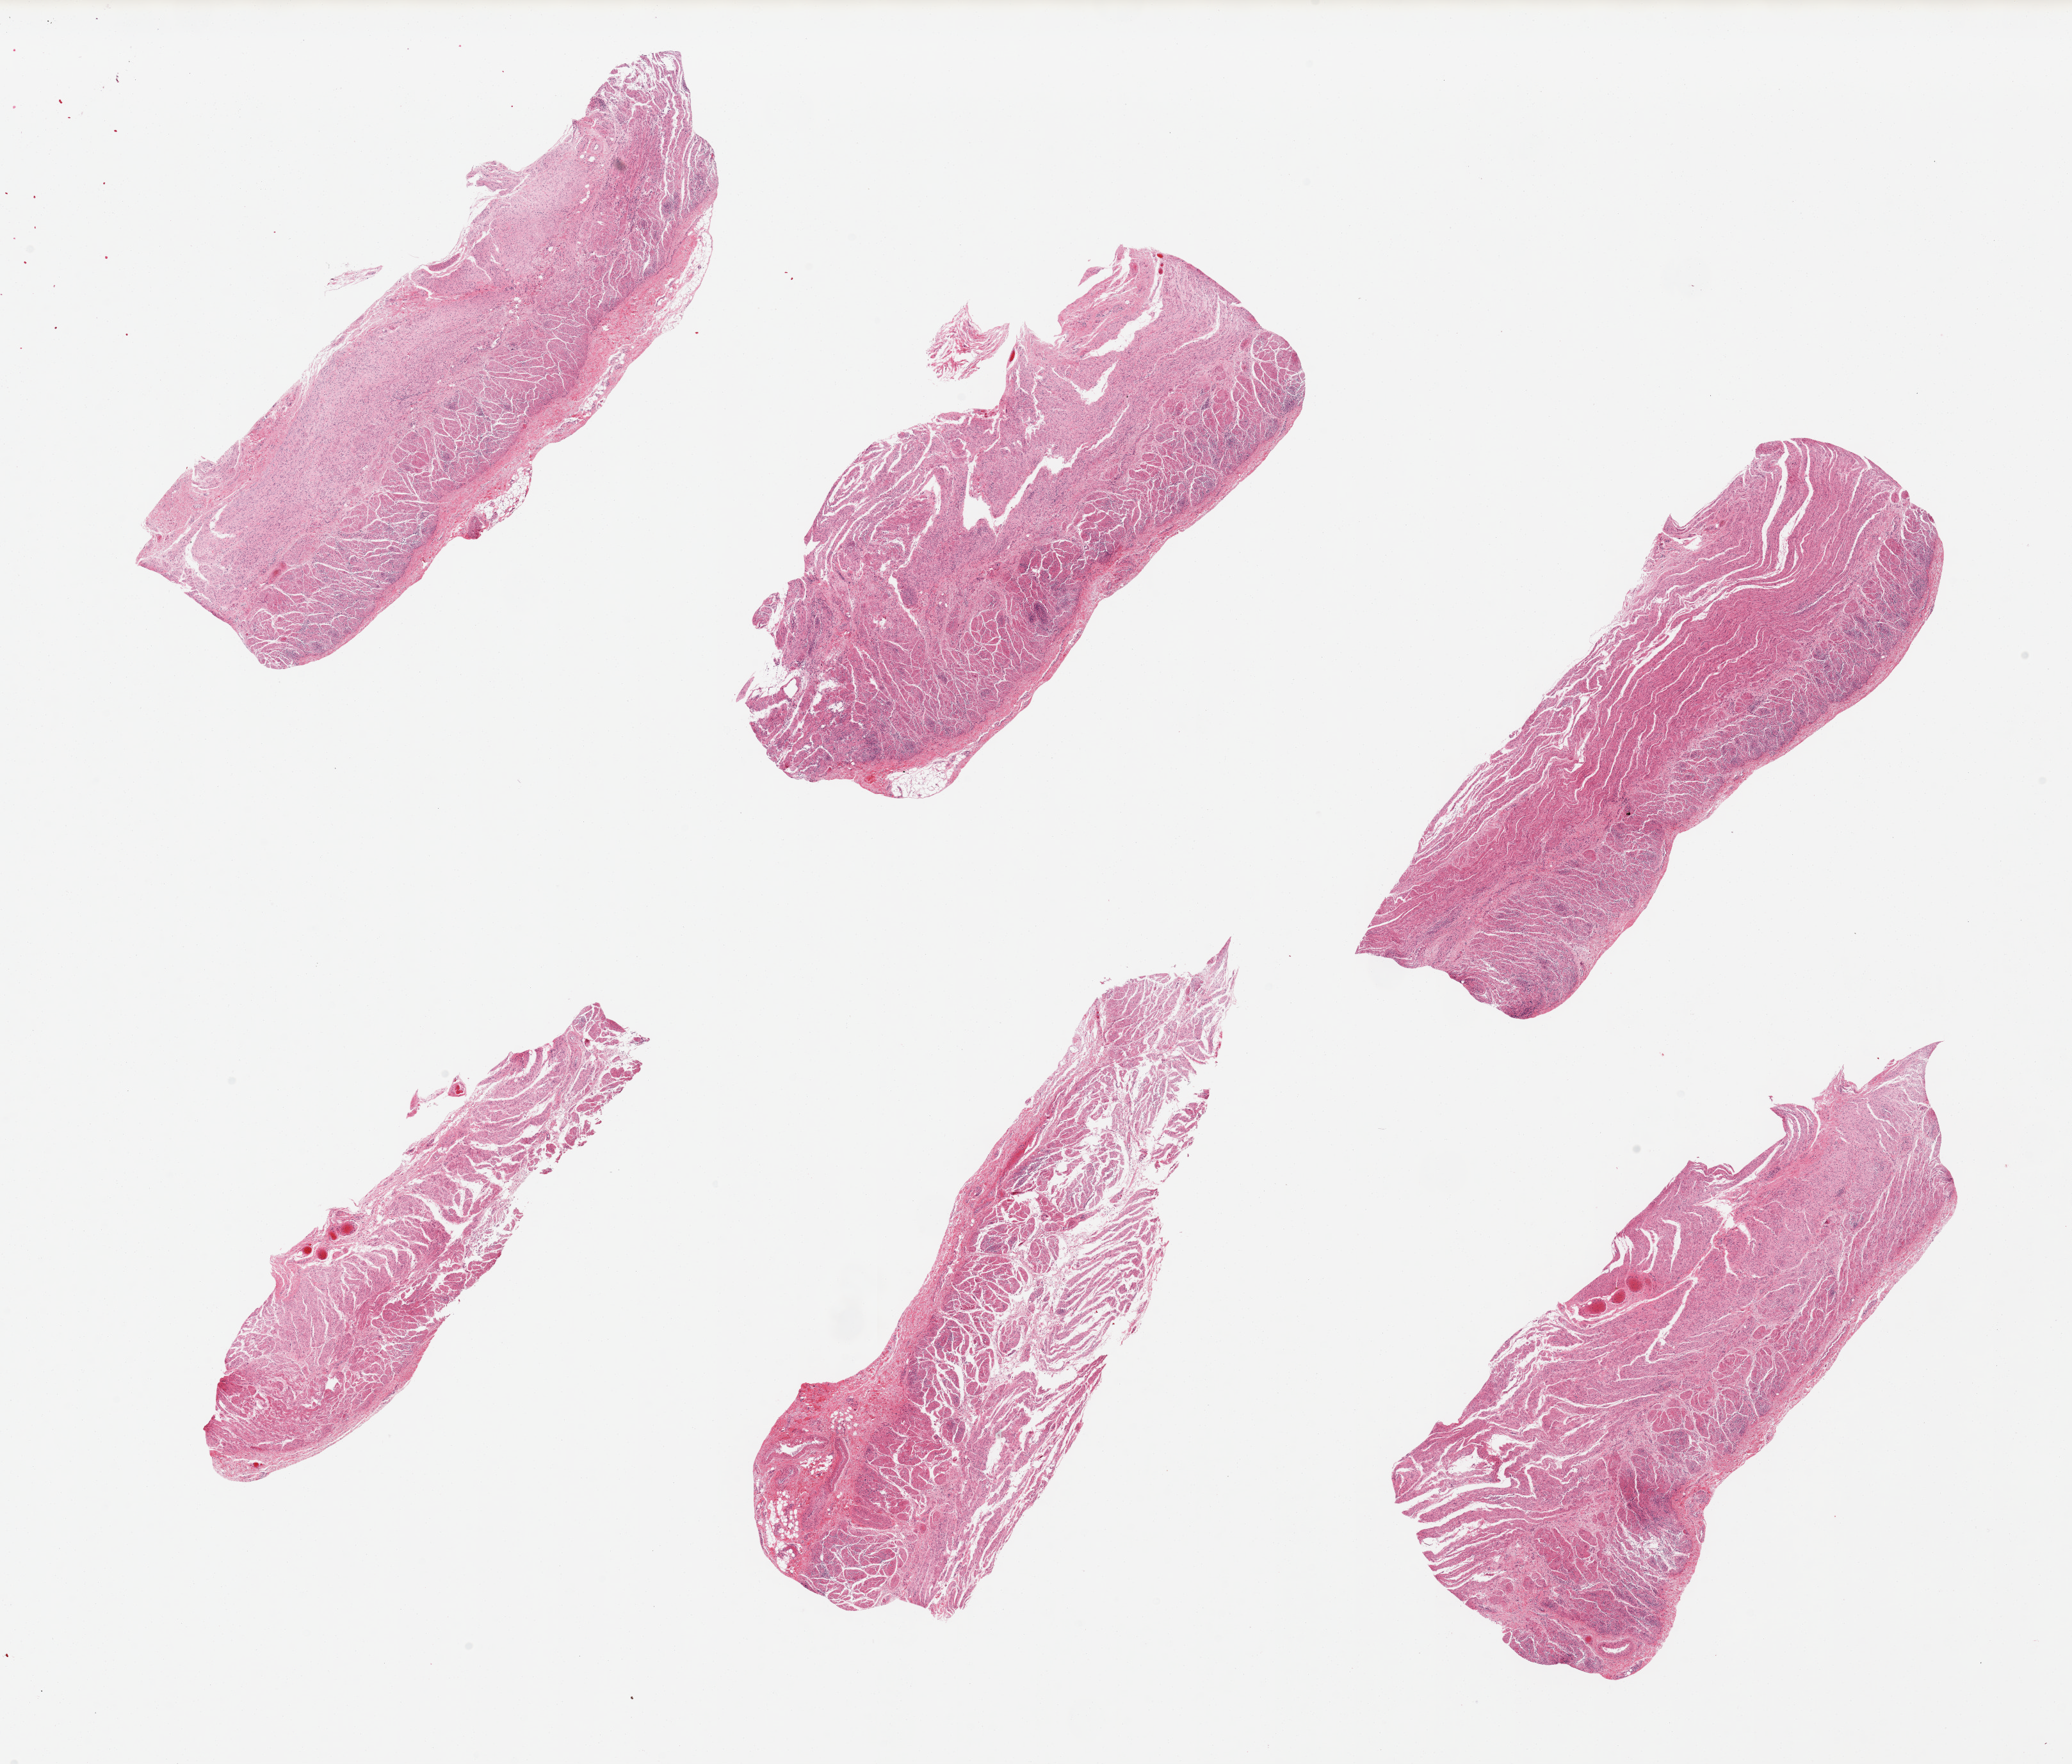
Whole-slide image, H&E stain — whole scanned area (about 25.6 x 21.8 mm, from a 20x scan) shown as a low-resolution overview, PAXgene-fixed paraffin-embedded (PFPE) section, section of gastroesophageal junction (target tissue), tissue donor sample.
* review note (as recorded): 6 pieces, all muscularis, good specimens